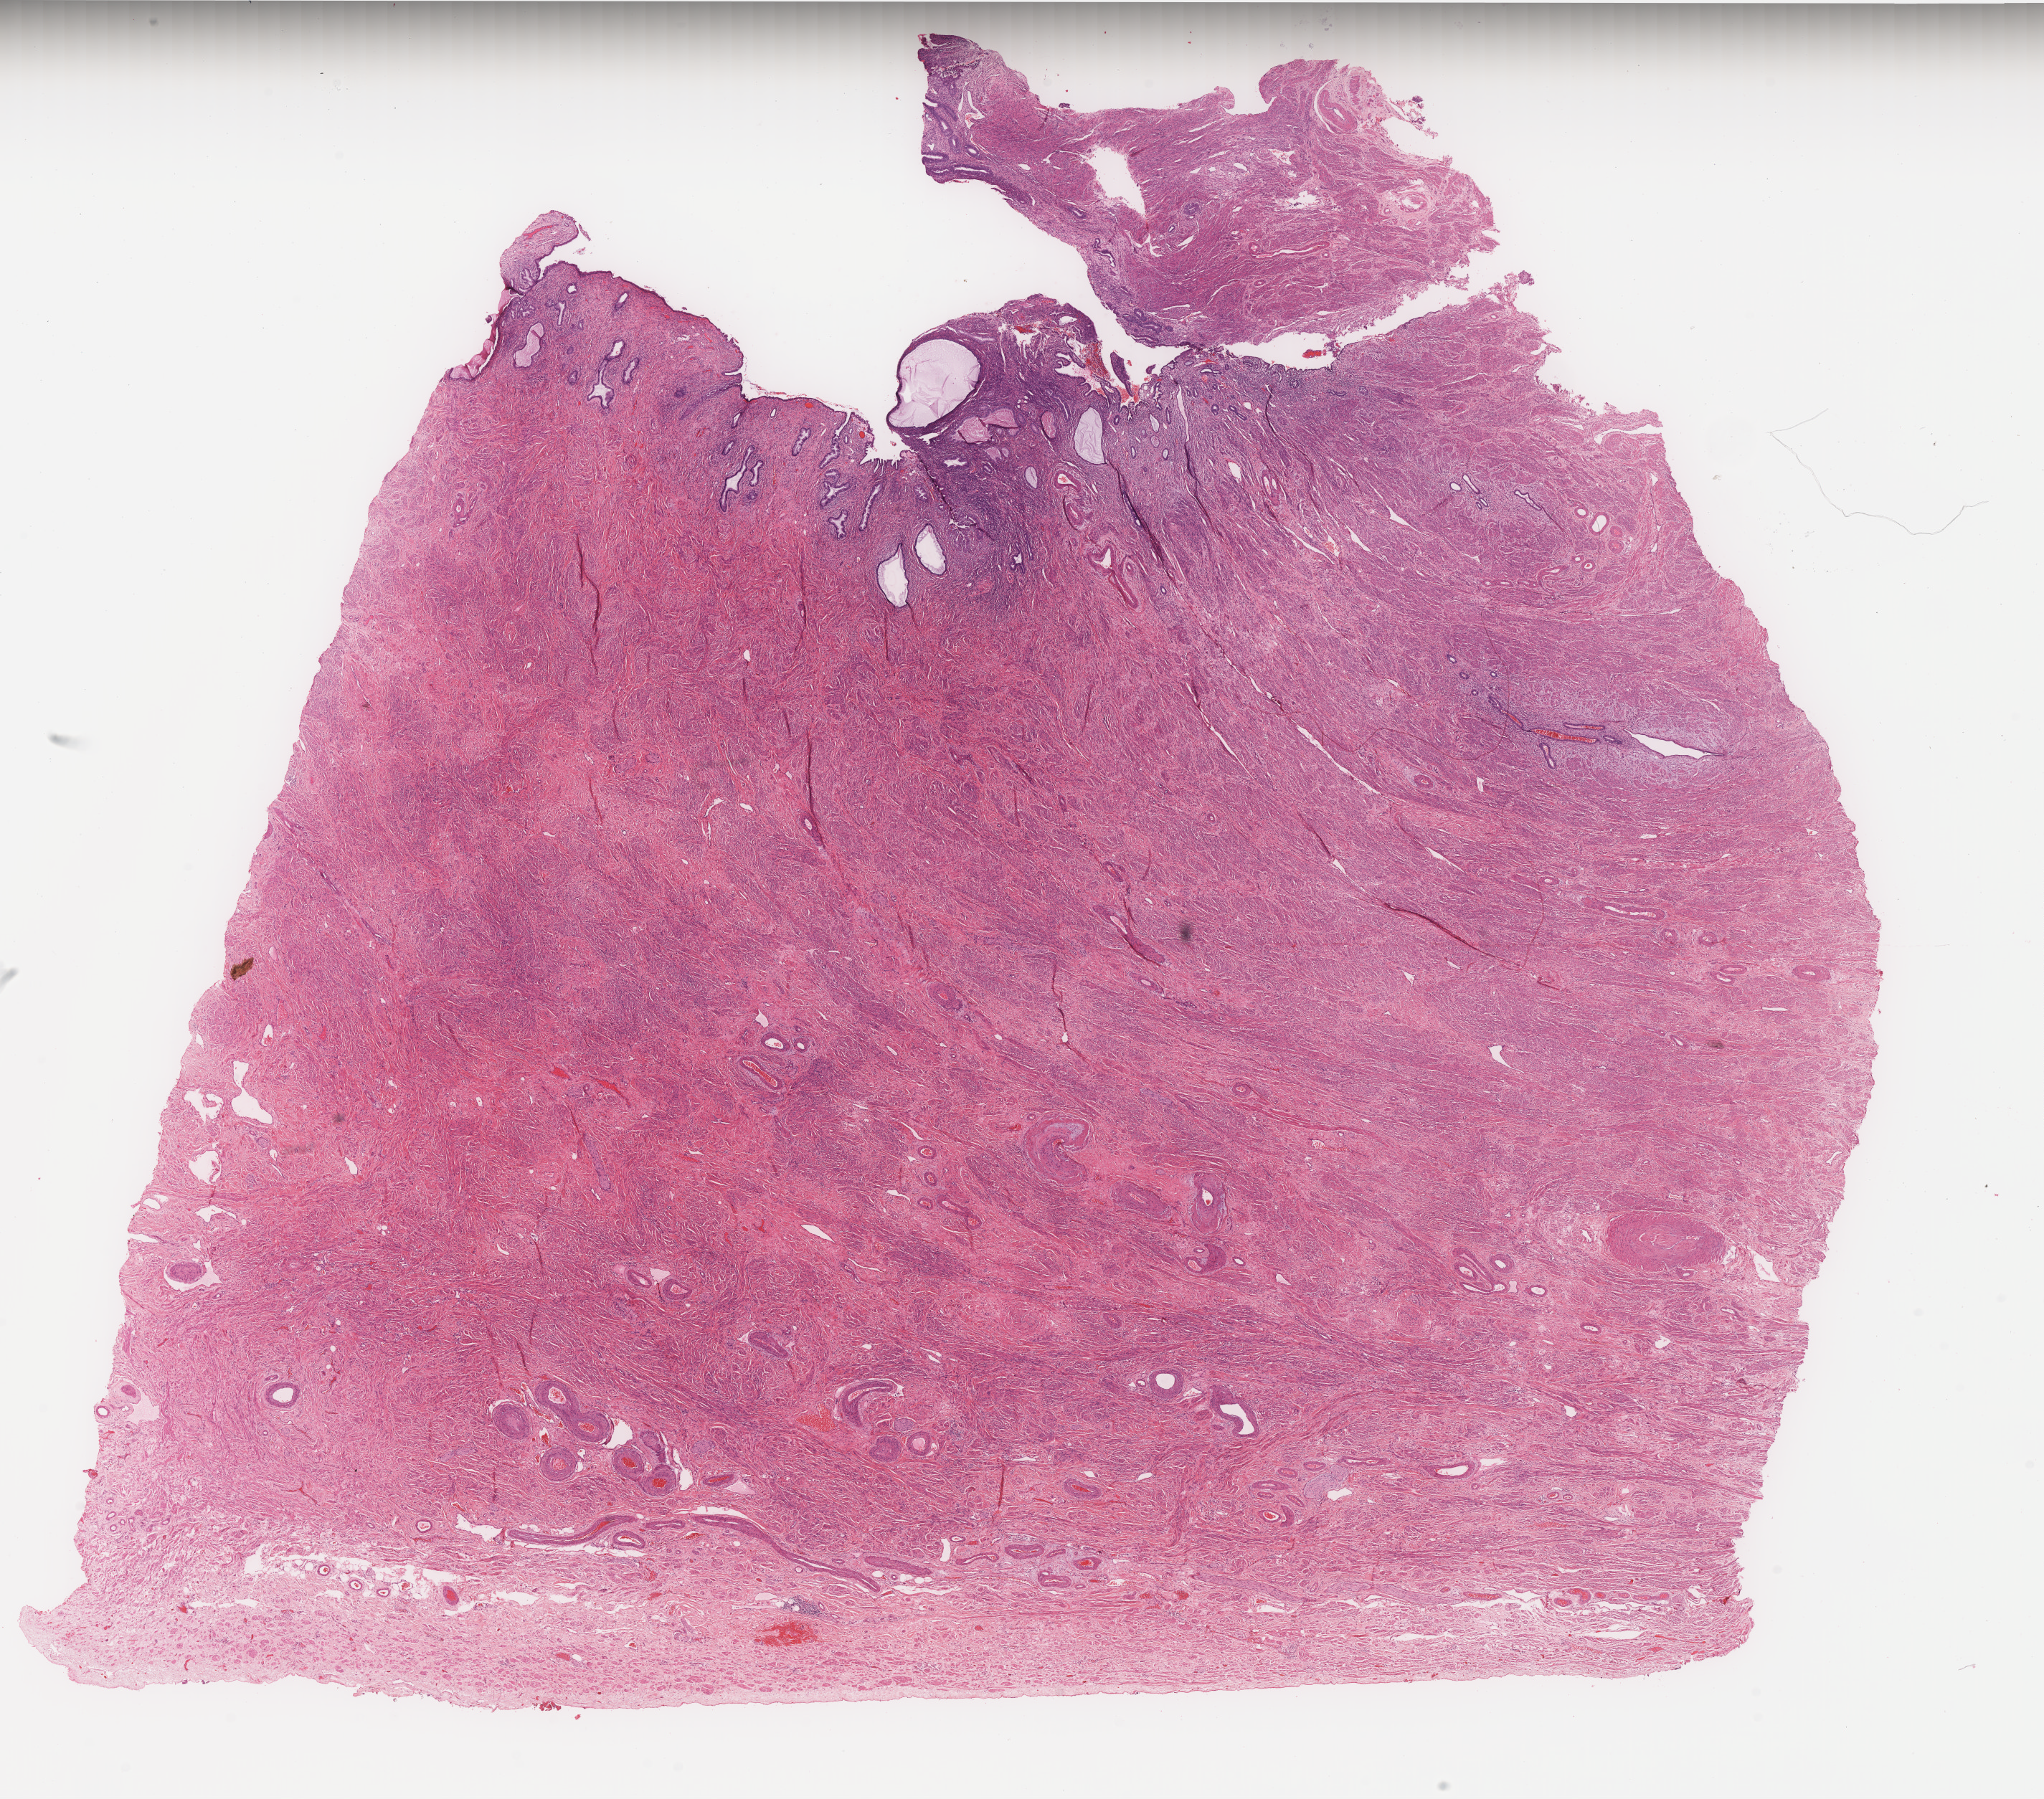
Digitized Hematoxylin and eosin (H&E) stained tissue section (whole slide) — shown as a low-resolution overview of the whole scanned area (about 22.8 x 20.1 mm, from a 40x scan), formalin-fixed paraffin-embedded (FFPE) diagnostic section, uterus, primary tumour sample. Patient: female, age at initial diagnosis 67 years. Histologic grade: G3 (poorly differentiated).
Pathologic diagnosis: Endometrioid adenocarcinoma, NOS (endometrium). FIGO stage: IIIC2.